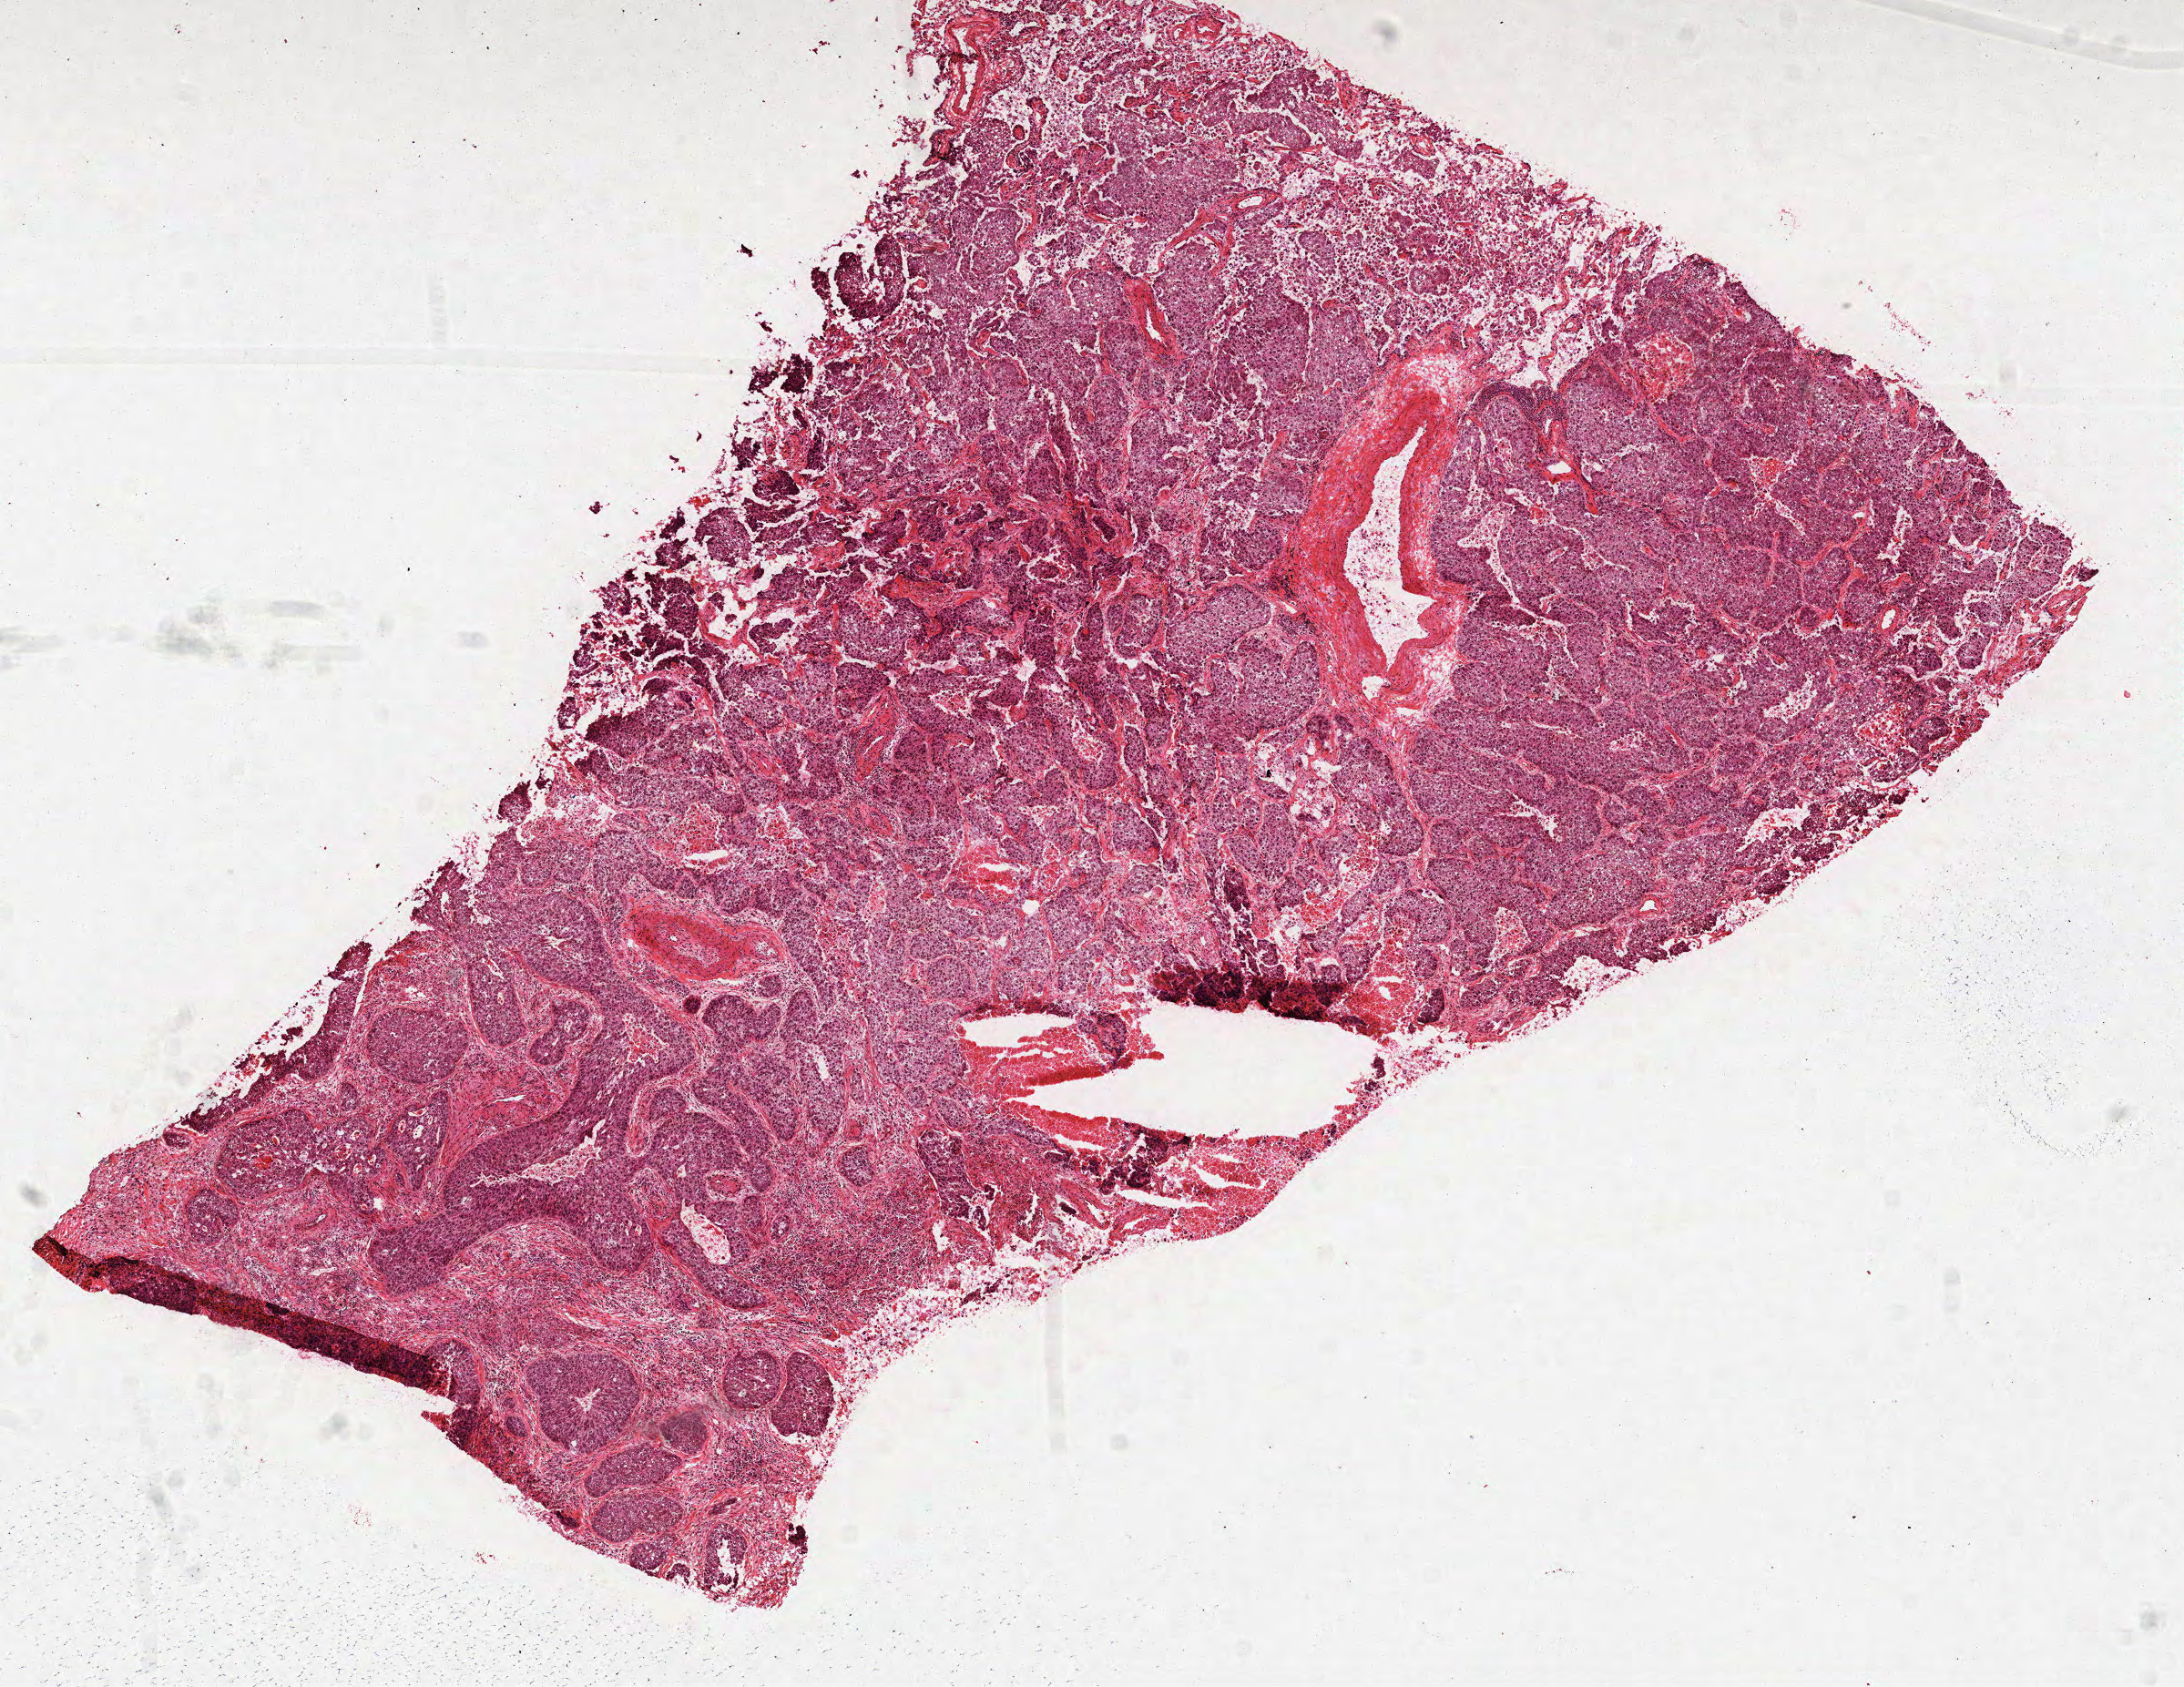
Whole-slide histology image, Hematoxylin and eosin (H&E) stained — a low-resolution overview of the entire scanned area, about 9.7 x 7.5 mm (acquisition: 40x scan); formalin-fixed paraffin-embedded (FFPE) diagnostic section; lung, primary tumour sample. Patient: male, age at initial diagnosis 80 years.
Diagnosis: Squamous cell carcinoma, NOS. Laterality: left. AJCC pathologic stage: IA (7th edition). TNM: T1b NX MX.